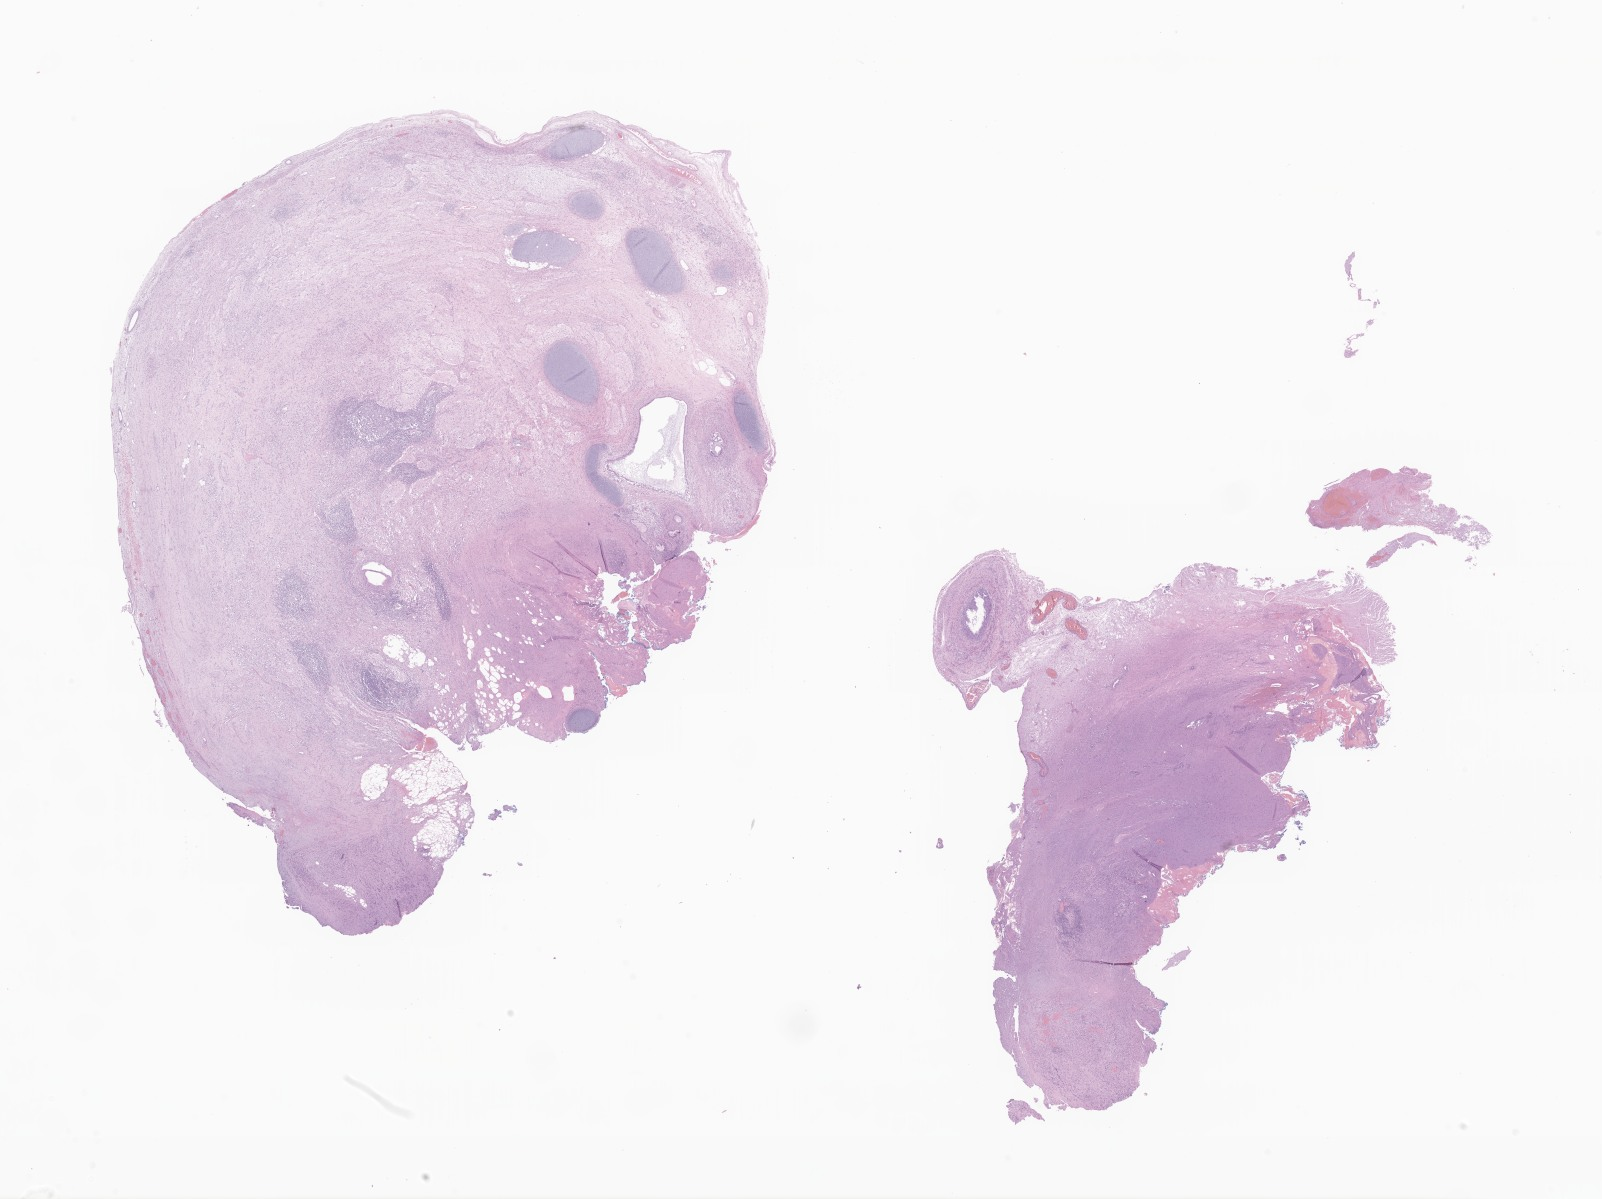
Whole-slide image, H&E stain of tumor tissue from the brain, whole scanned area (about 27.0 x 20.2 mm) shown as a low-resolution overview, formalin-fixed paraffin-embedded section. Patient male; age 235 months (19 years 7 months).
Diagnosis (ICD-O-3 morphology term): Mixed germ cell tumor.